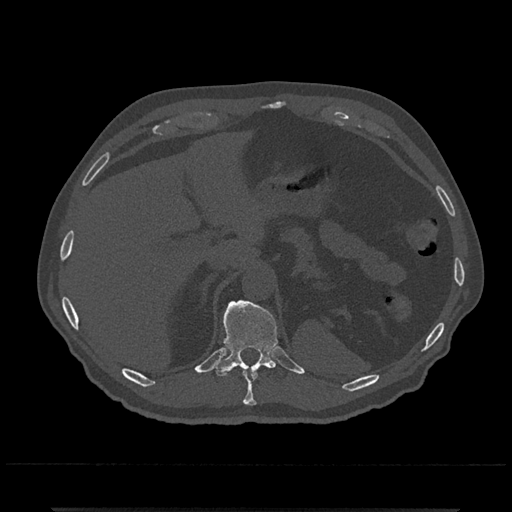
CT including the spine, one axial slice; position 509 of 797 along the scan axis; reconstruction kernel Br40s/3; bone window (W 1800 / L 400 HU); 512 × 512 image matrix. Male patient, age 67 years. Case-level facts recorded for this patient, not image findings: primary cancer: prostate.
Structures marked on this image (semi-automatic segmentation, software-assisted and operator-edited):
- T10 vertebra: bounding box (x1, y1, x2, y2) in pixels: (243, 372, 257, 406)
- T11 vertebra: (214, 300, 282, 377)